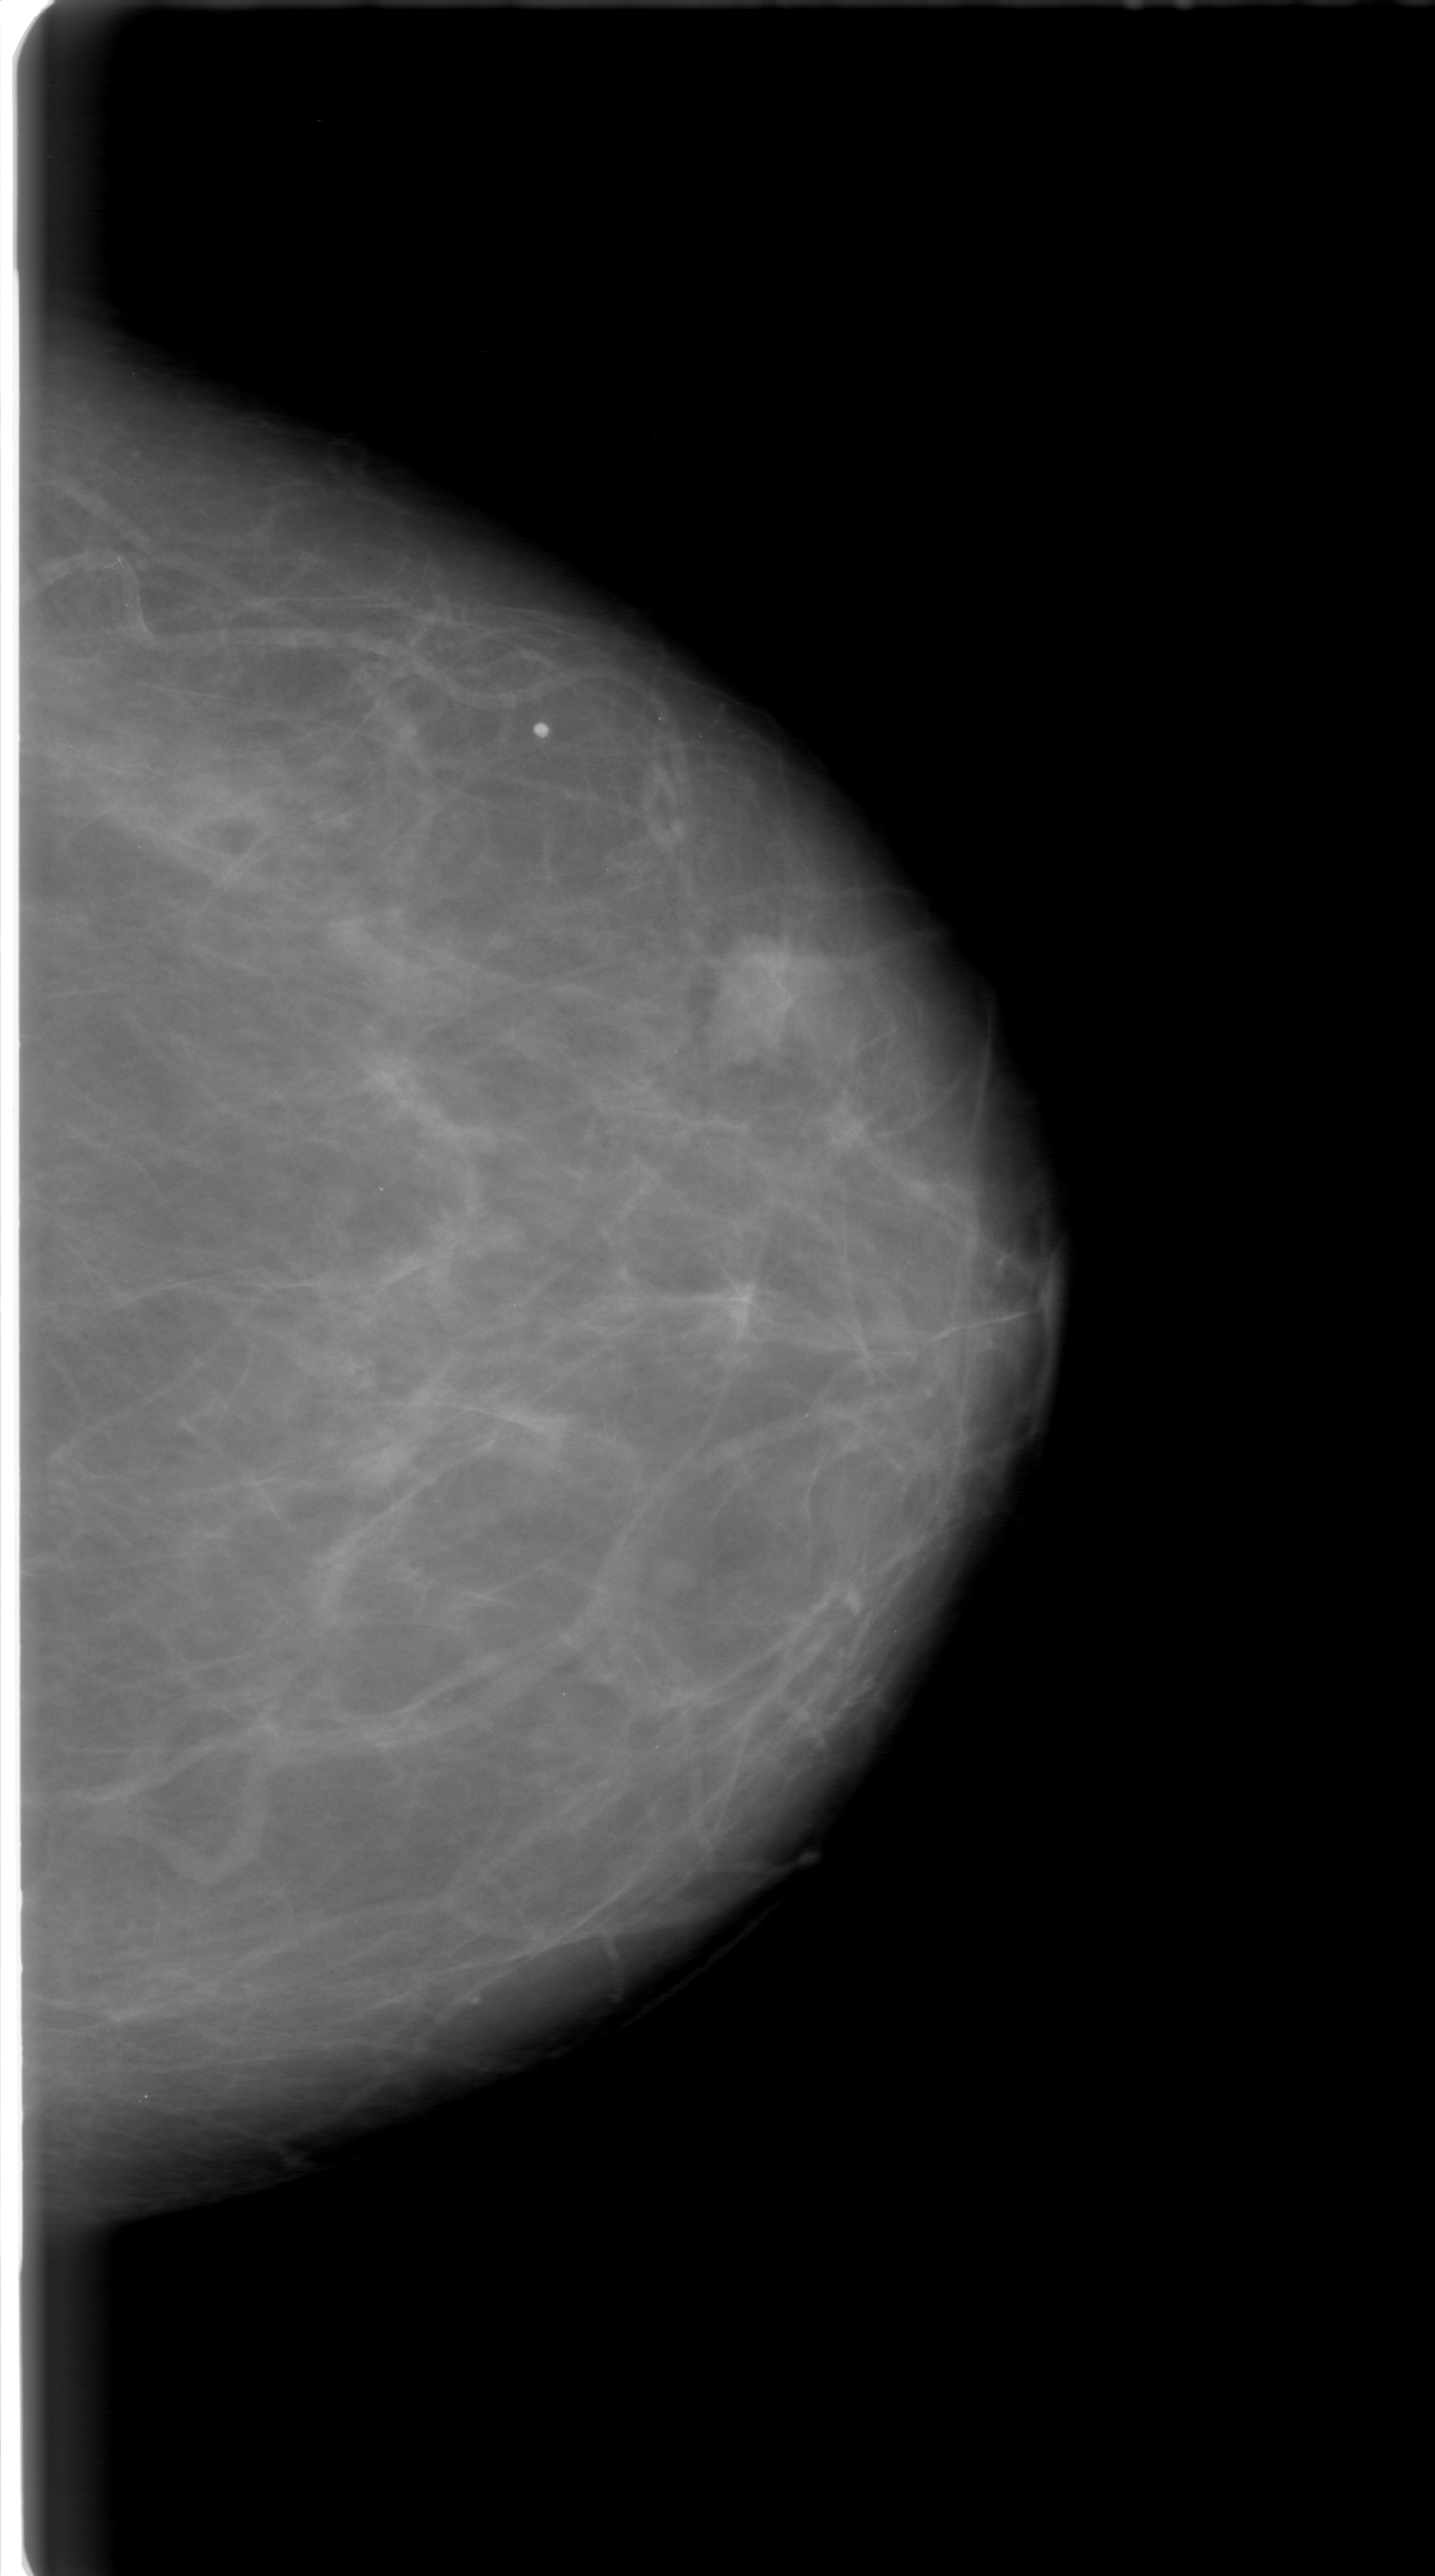
Scanned film-screen mammogram. Left breast. Craniocaudal (CC) view. Breast composition: almost entirely fatty (BI-RADS density category 1 of 4). 1435 × 2576 image matrix.
Expert-marked regions of interest on this image (one box per marked abnormality):
- mass, shape lobulated, margins obscured; BI-RADS assessment category 0; subtlety rating 5 on a 1 (subtle) to 5 (obvious) scale; pathology (as recorded): benign: bounding box [x1, y1, x2, y2] px = [694, 927, 862, 1122]